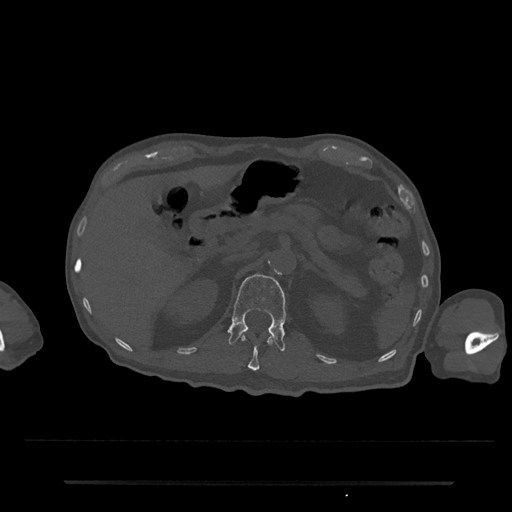
CT including the spine, one axial slice; position 152 of 797 along the scan axis; reconstruction kernel Br40s/3; 120 kVp; bone window (W 1800 / L 400 HU); 0.5 mm slice thickness; 512 × 512 image matrix, field of view 427 × 427 mm. Patient: male, 74 years. From the clinical record (not read from this slice): primary cancer: prostate.
Structures marked on this image (semi-automatically segmented with operator editing):
- L1 vertebra: bounding box (x1, y1, x2, y2) in pixels: (228, 274, 286, 352)
- T12 vertebra: (241, 335, 273, 371)